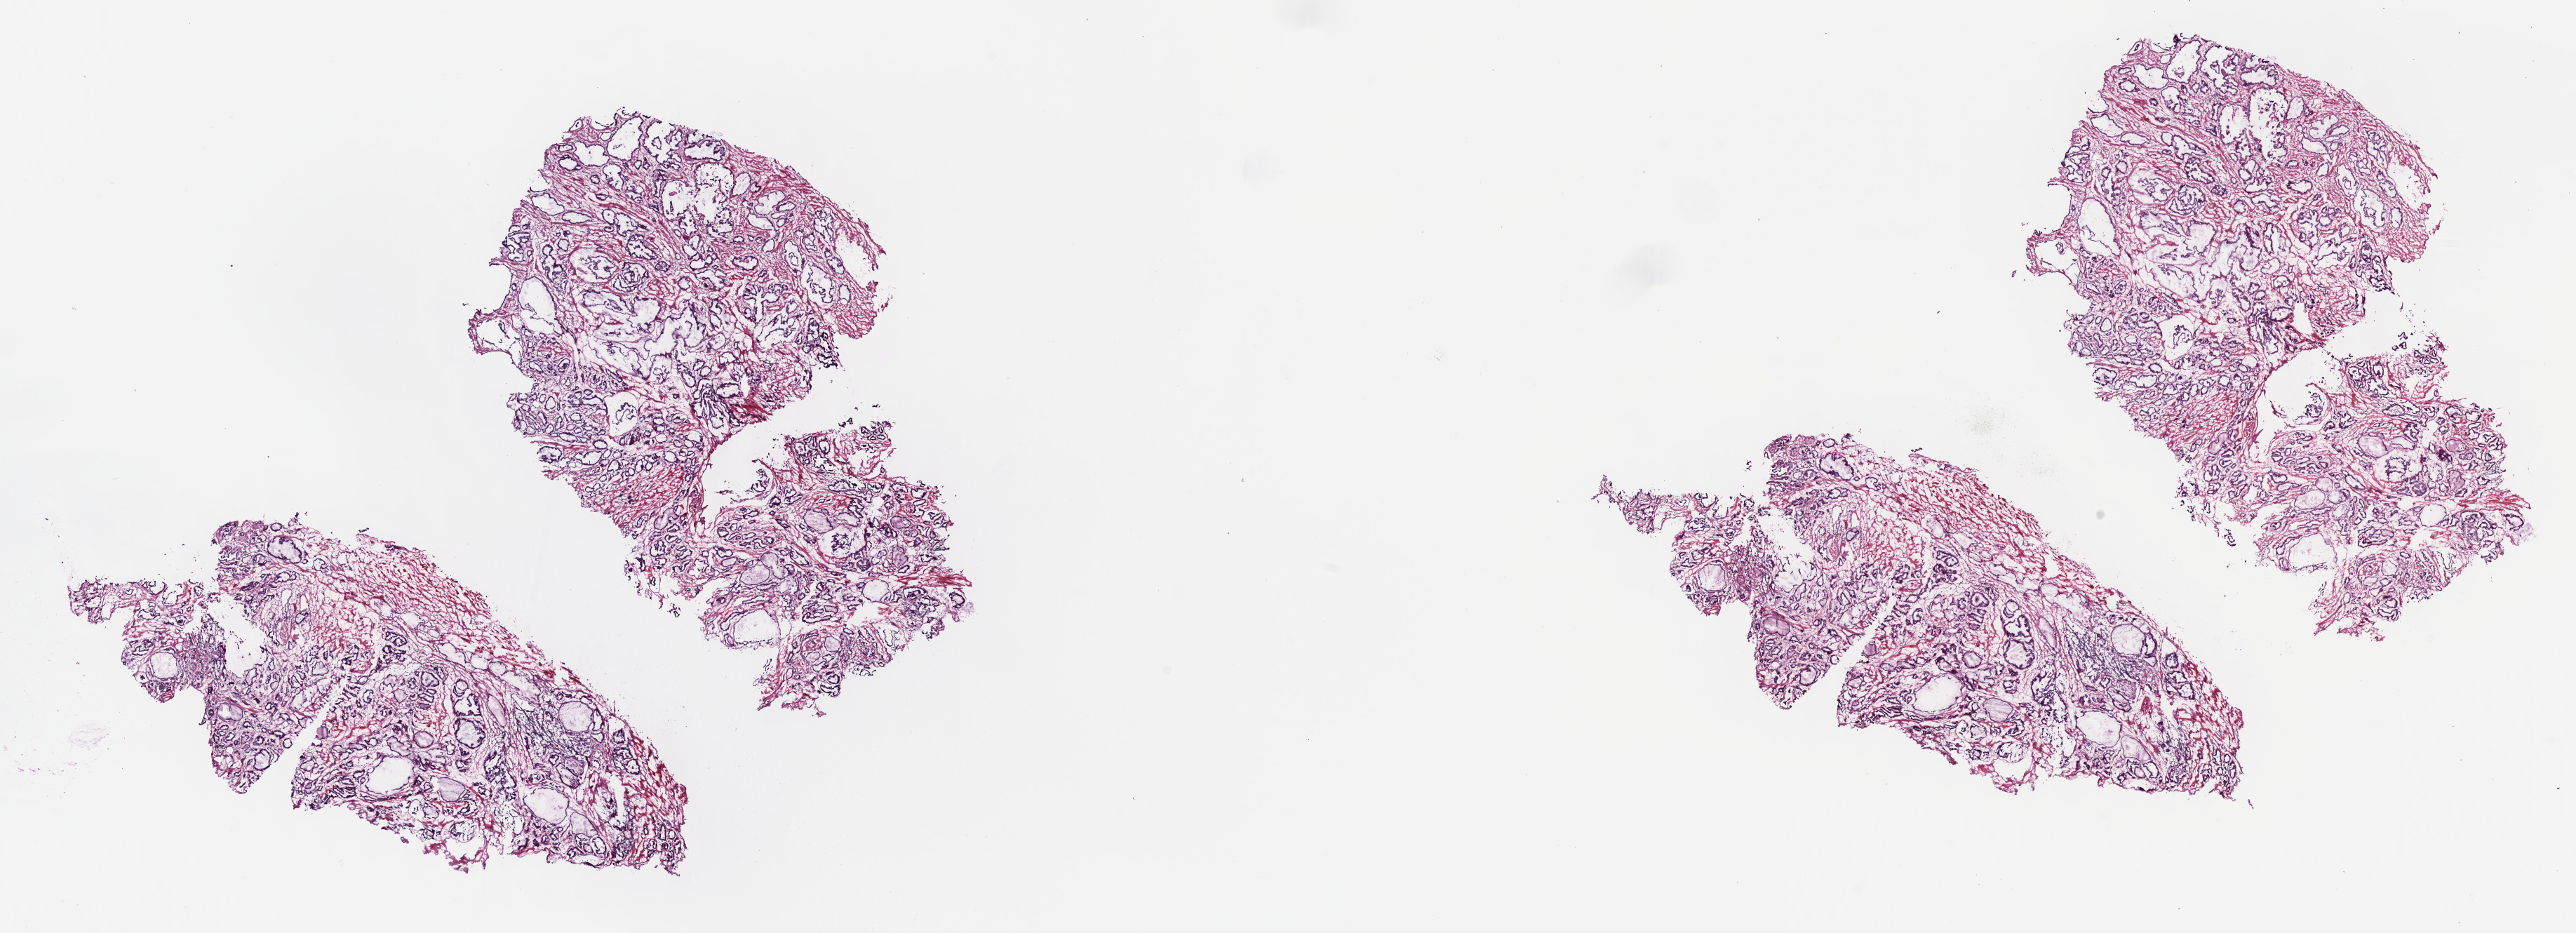
Whole-slide histology image, Hematoxylin and eosin (H&E) stained, shown as a low-resolution overview of the whole scanned area (about 29.7 x 10.8 mm), frozen section from the top of the tissue portion, sample: primary tumour, prostate. Patient: male, age at initial diagnosis 49 years. Gleason score: 7 (3+4). Slide review estimates, as recorded: tumour cells 70%, tumour nuclei 70%, normal cells 0%, stromal cells 30%, necrosis 0%. Infiltration values recorded for this section: lymphocyte infiltration 60%, monocyte infiltration 10%, neutrophil infiltration 20%.
Lymph nodes positive (case pathology): 0 of 34 examined. Histologic diagnosis: Adenocarcinoma, NOS (prostate gland).